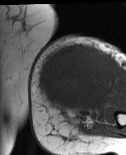
MRI of an extremity soft-tissue mass, one axial slice; position 25 of 86 along the scan axis; MR volume resampled by the dataset authors to the PET/CT grid (not the native acquisition matrix); 126 × 155 image matrix, field of view 123 × 151 mm. Female patient. From the clinical record (not read from this slice): histological type: pleiomorphic leiomyosarcoma; grade: high; site of the primary tumour: left biceps.
Outlined on this slice (expert contour drawn on MRI and transferred to this co-registered scan by the dataset authors):
- gross tumour volume including surrounding oedema: bounding box [x1, y1, x2, y2] px = [38, 44, 117, 116]
- gross tumour volume (mass): [38, 44, 117, 112]